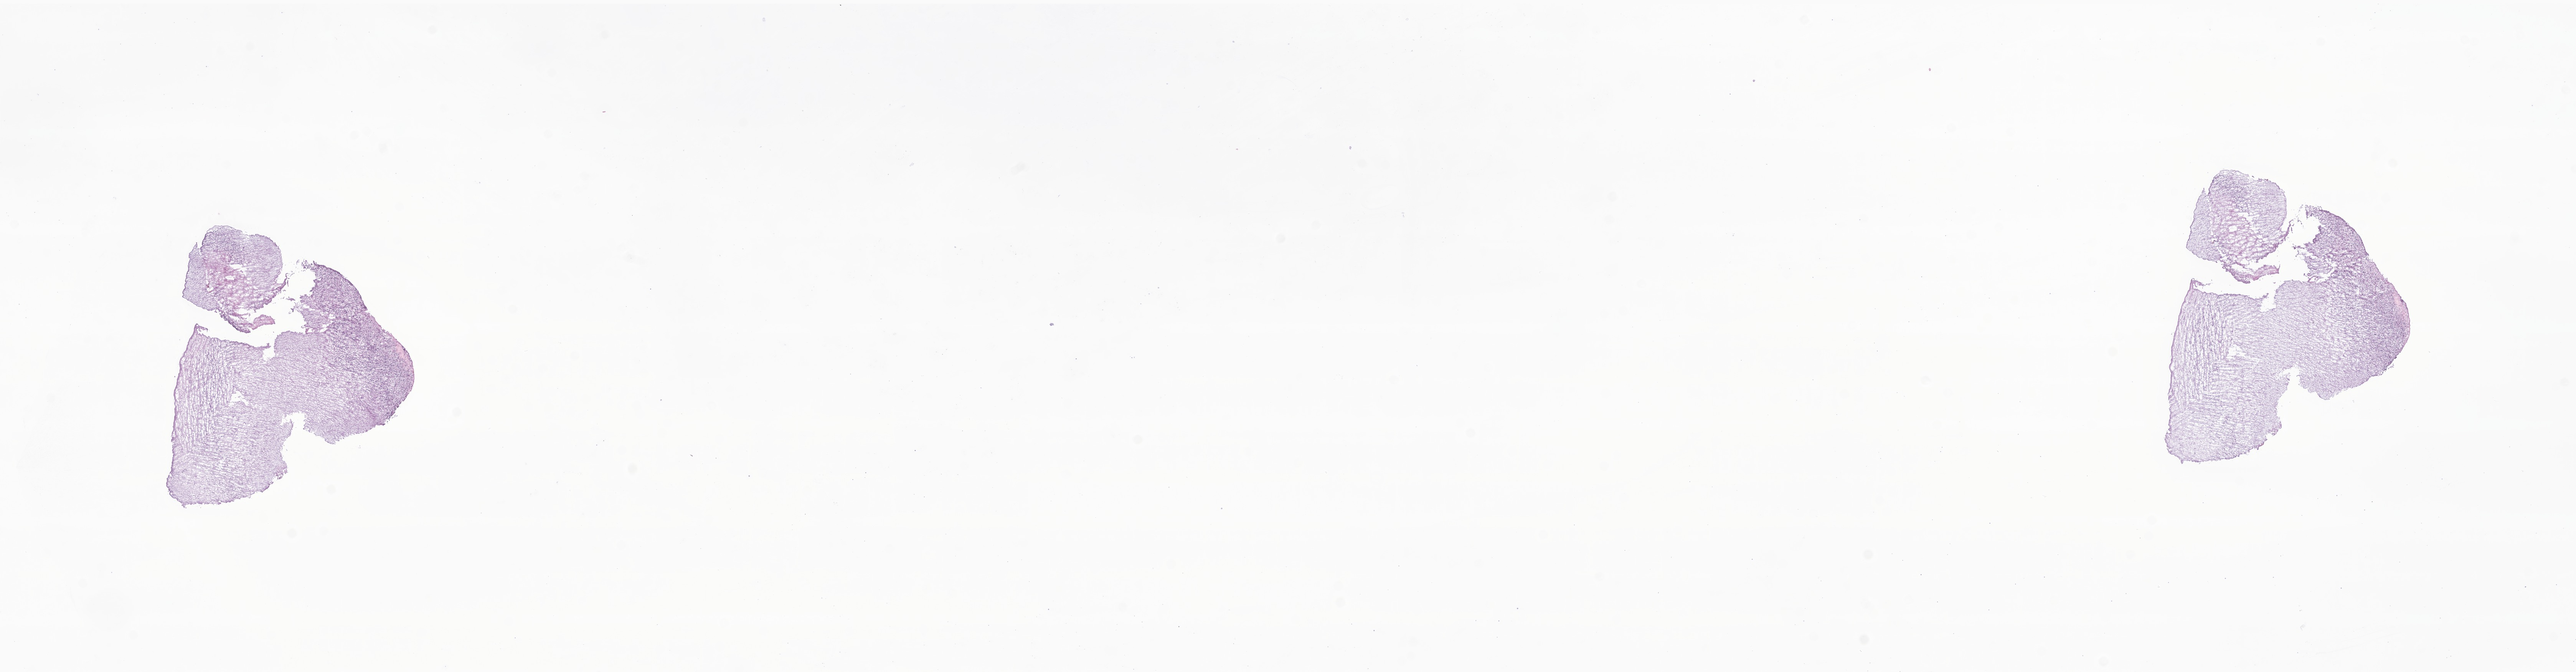
Haematoxylin and eosin whole-slide image of tumor tissue from the cerebellum, whole scanned area (about 28.3 x 7.4 mm) shown as a low-resolution overview; frozen section. Patient male; age 777 days (about 2.1 years).
Diagnosis (ICD-O-3 morphology term): Pilocytic astrocytoma.